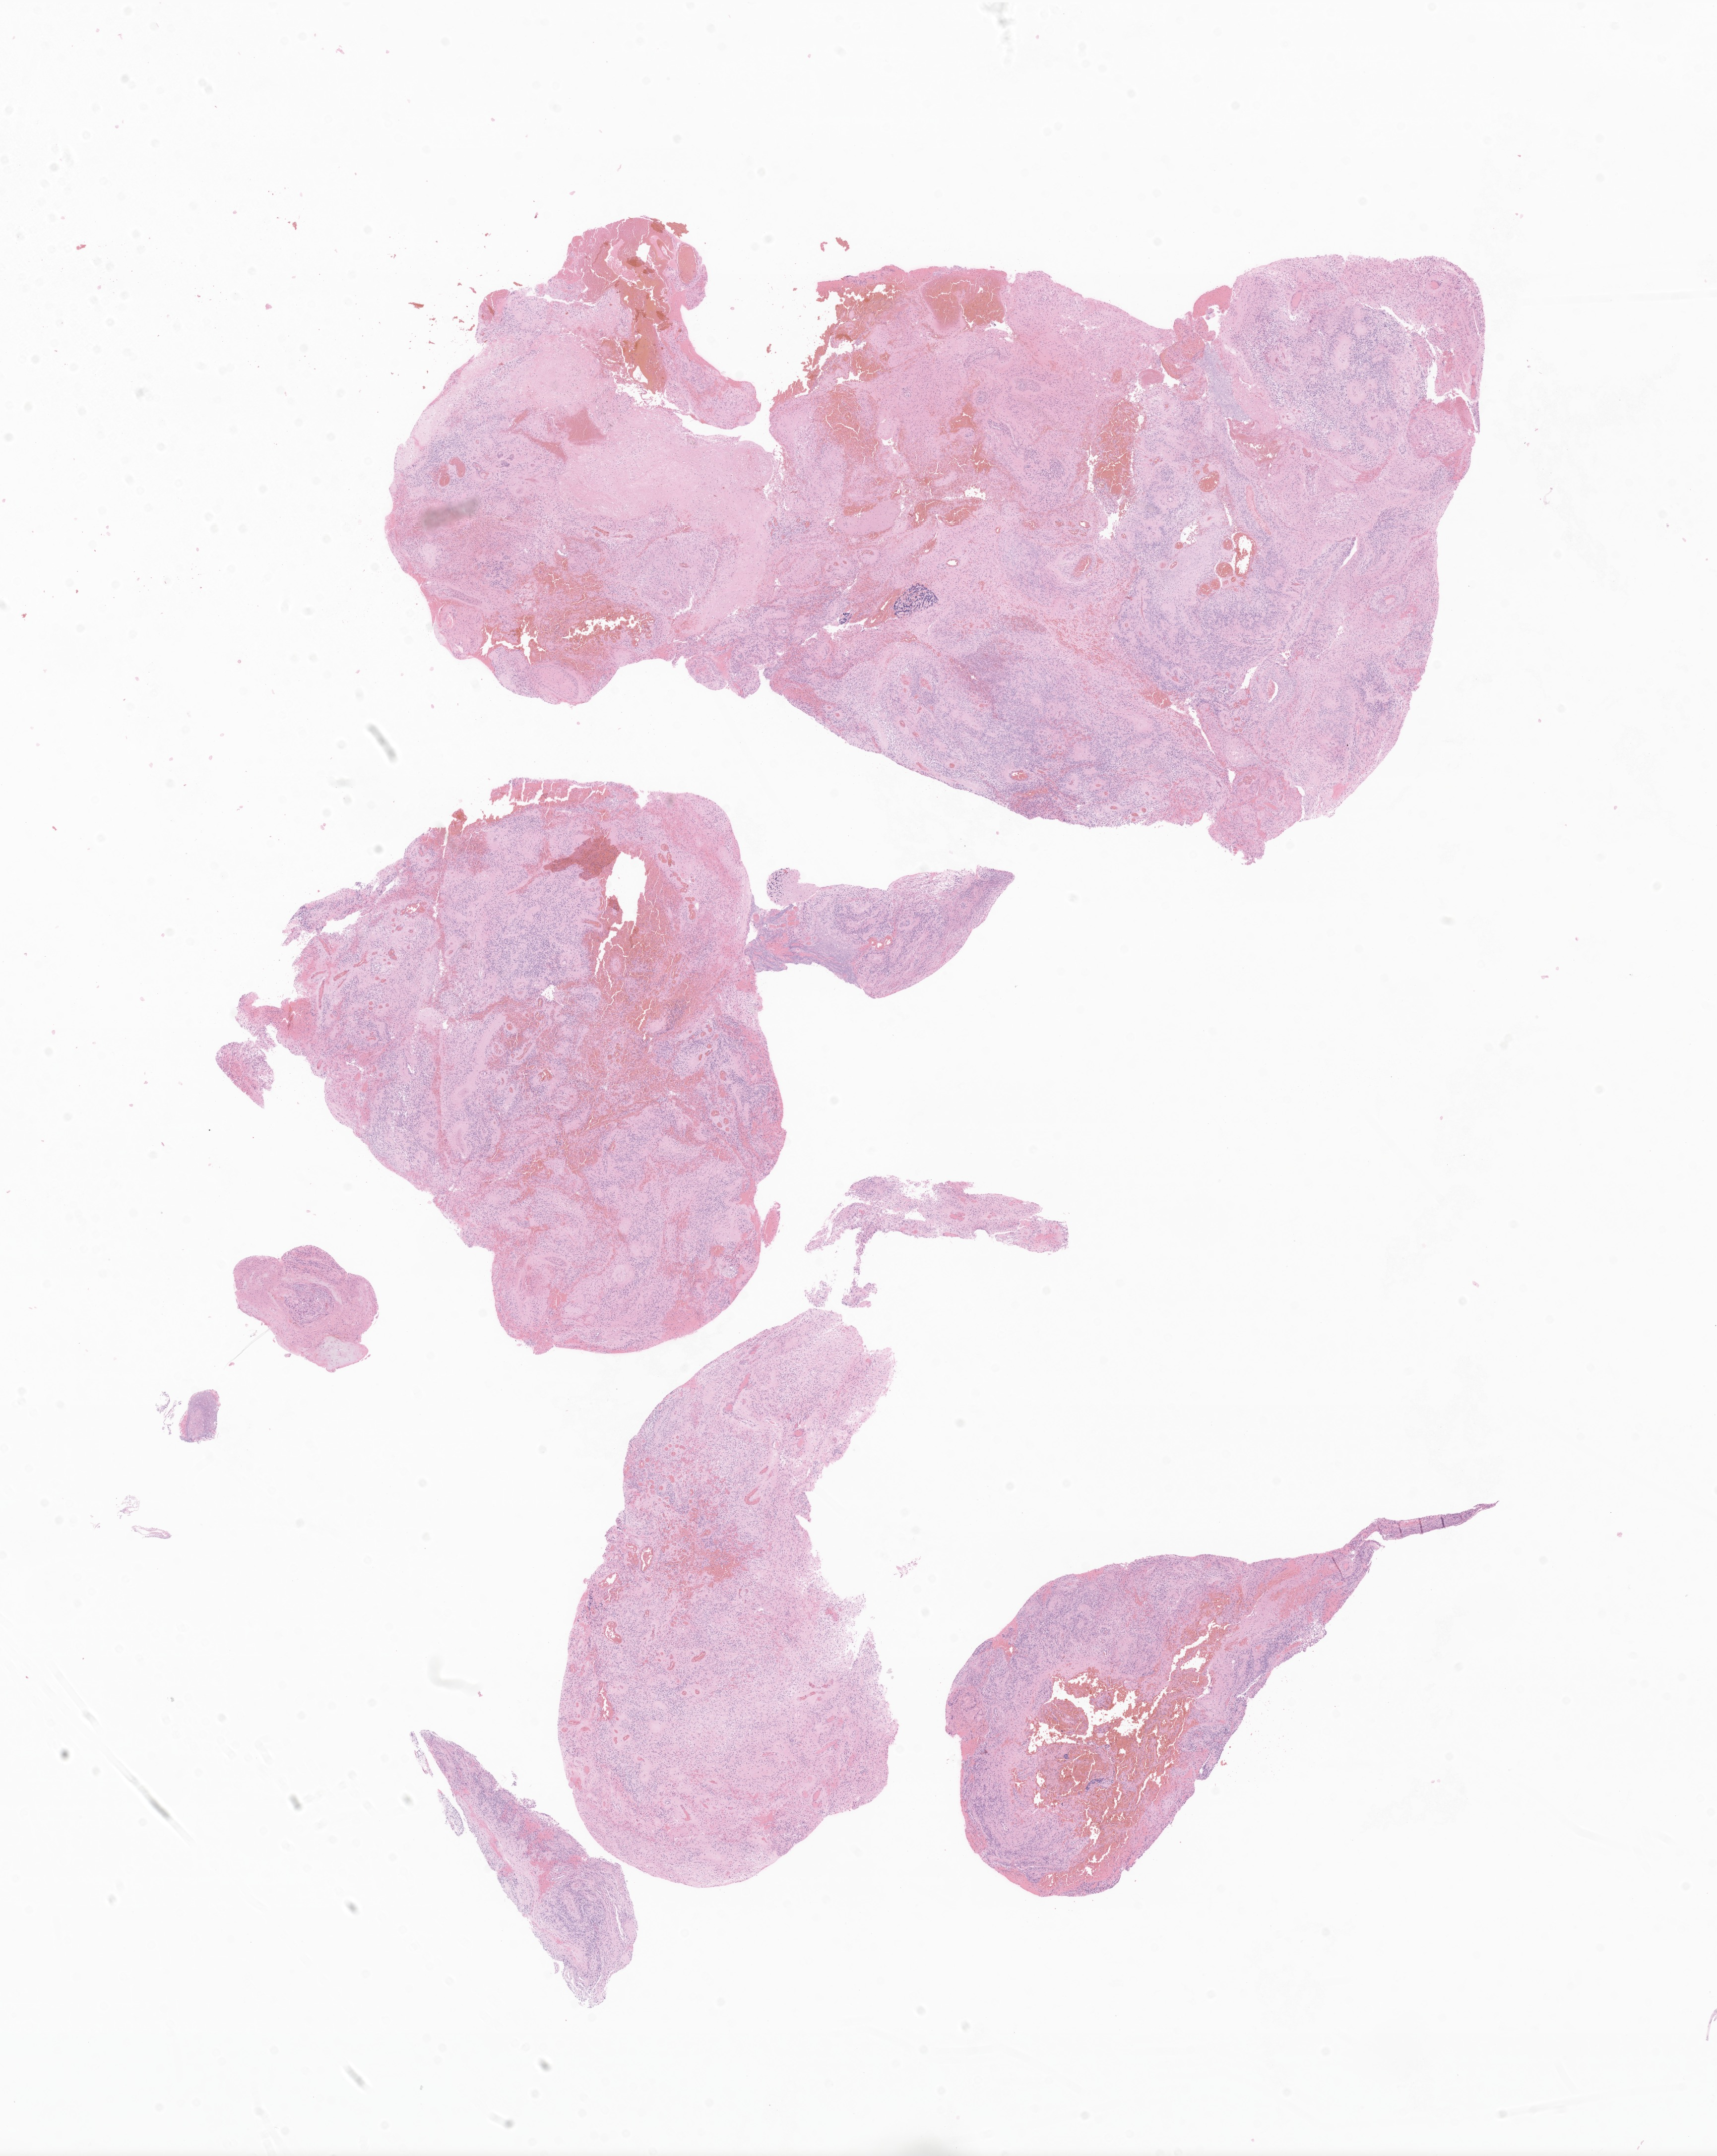
Hematoxylin and eosin (H&E) whole-slide image of tumor tissue from the brain — a low-resolution overview of the entire scanned area, about 14.6 x 18.3 mm; FFPE section. Patient: female, age 103 months (8 years 7 months).
Diagnosis: Ependymoma, NOS.